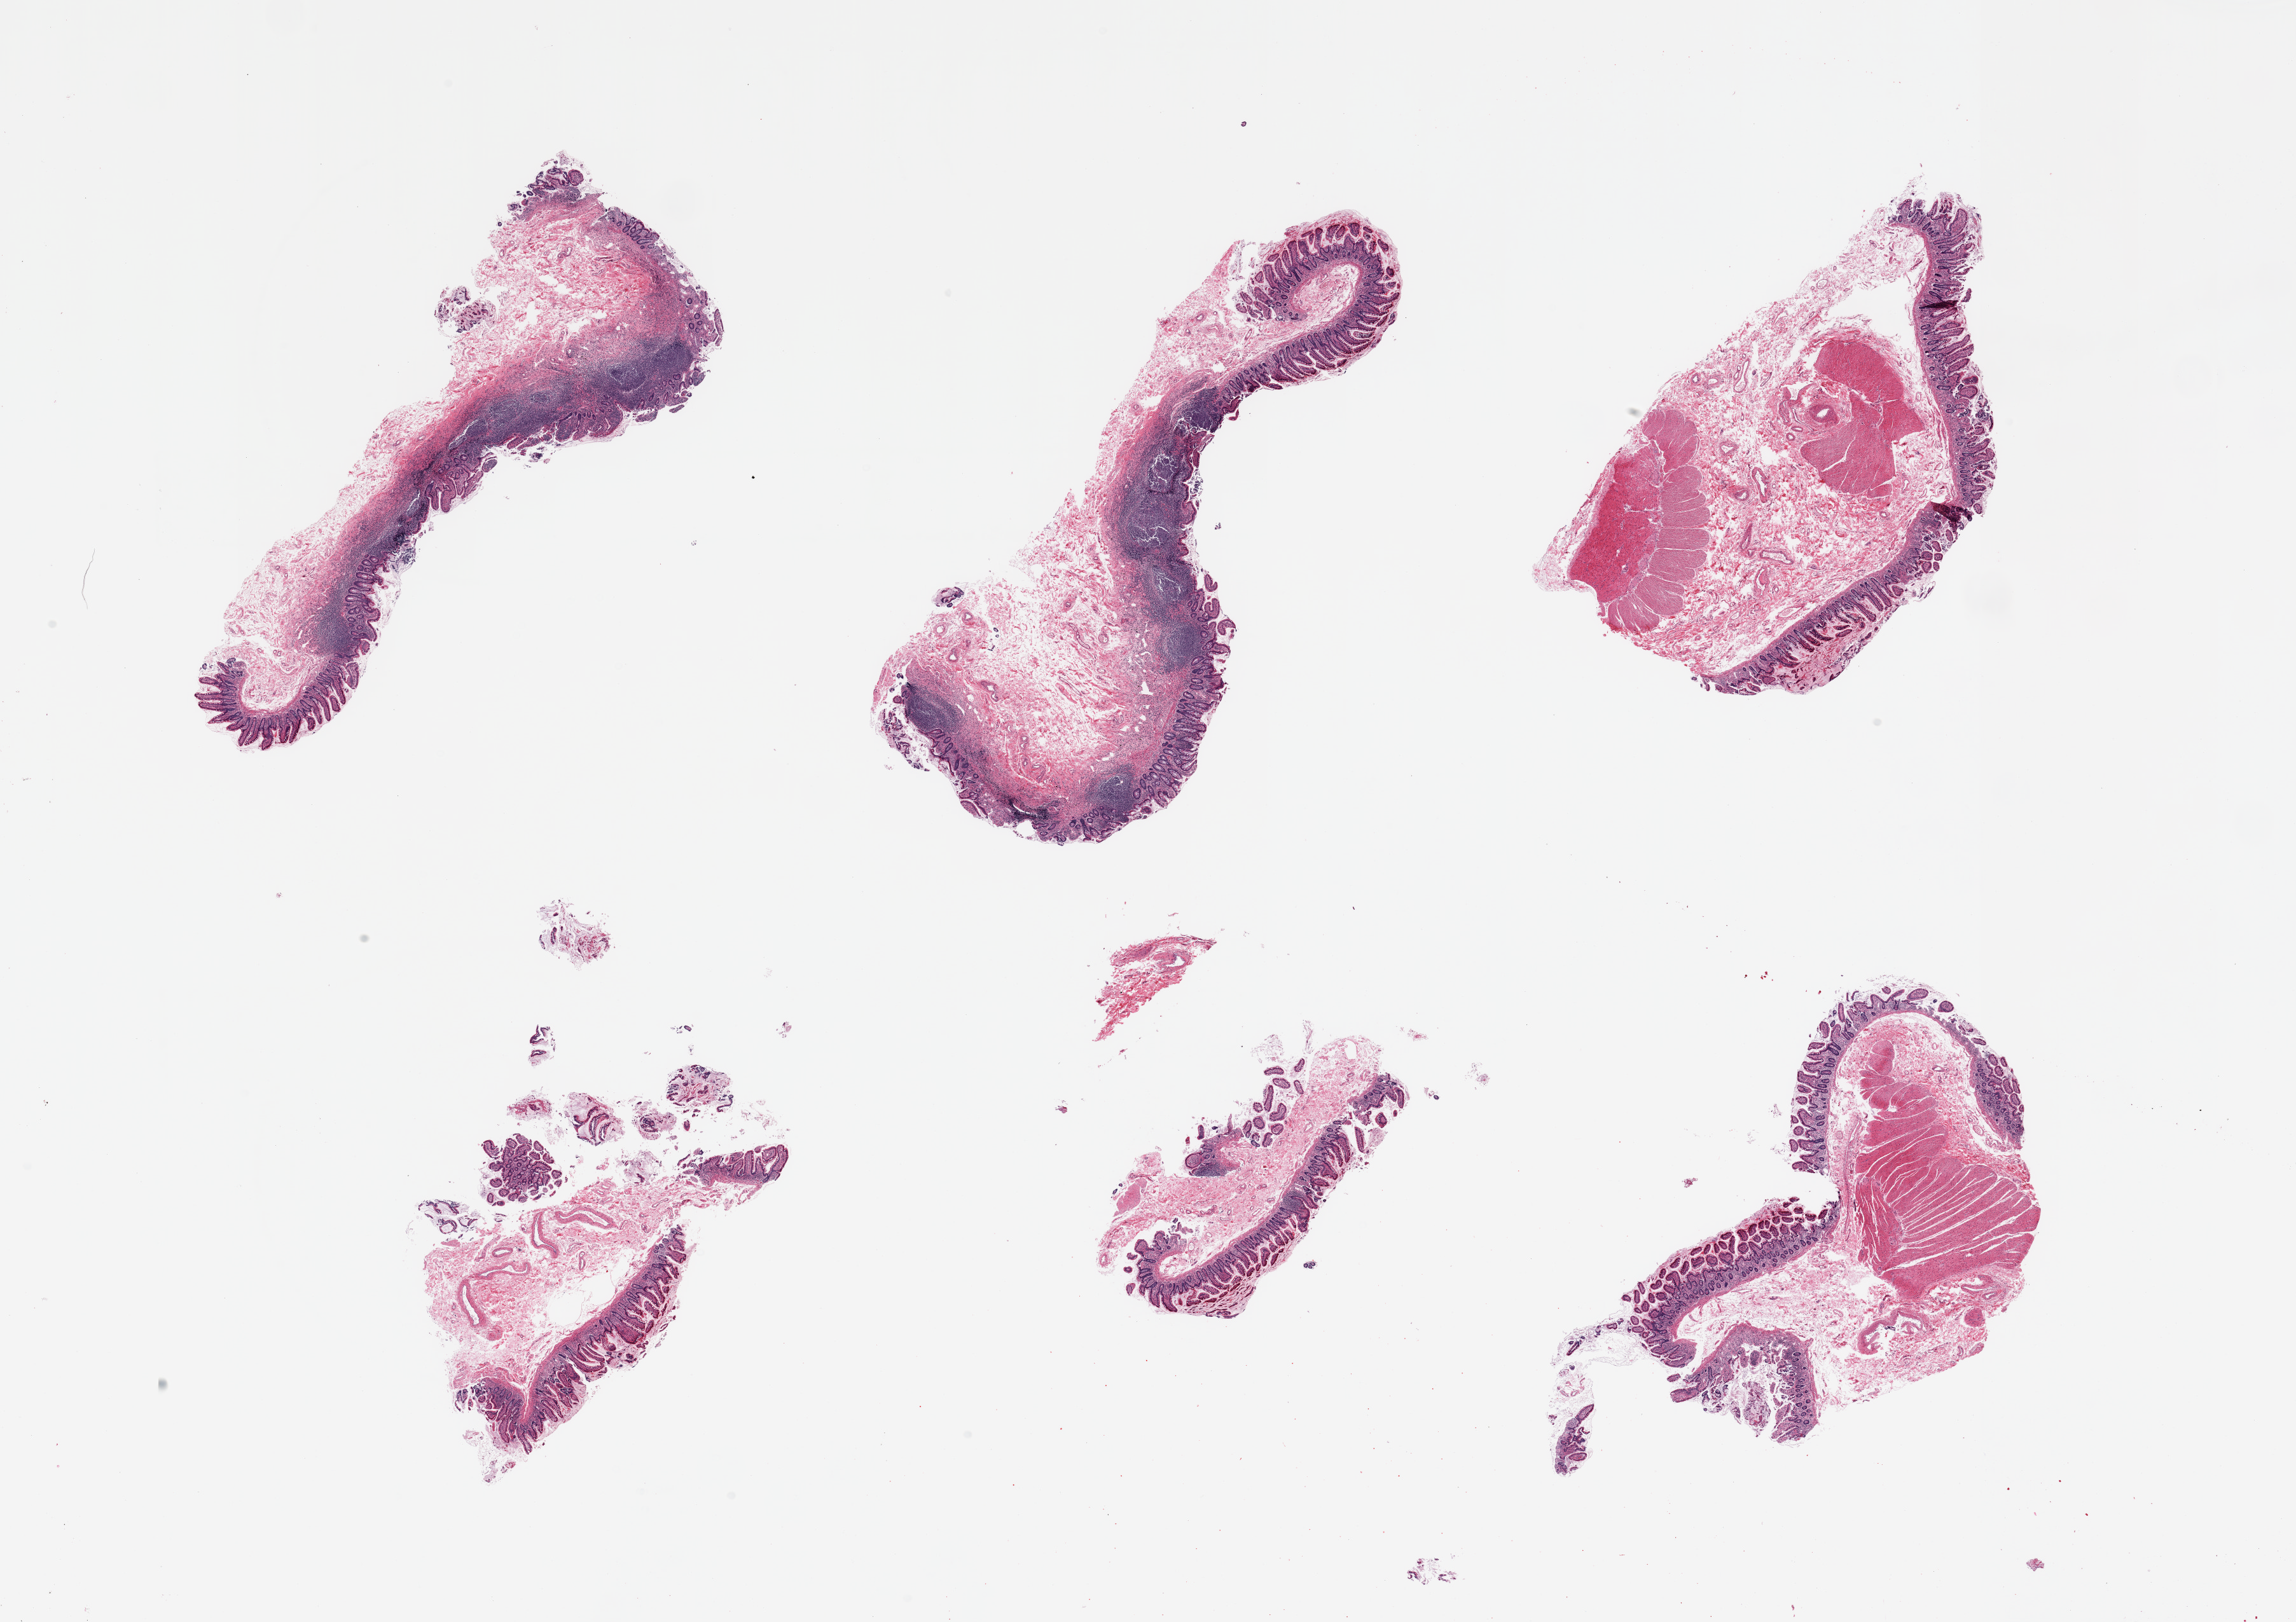
Digitized haematoxylin and eosin-stained section, brightfield — shown as a low-resolution overview of the whole scanned area (about 28.5 x 20.2 mm, acquisition: 20x scan). PAXgene-fixed, paraffin-embedded tissue. Sampled site (target tissue): ileum. Tissue donor sample. Donor sex: male.
Pathologist's review note for this sample: 6 pieces; fragments of mucosa with good, but variable, lymphoid tissue, few with residual muscularis (not target).